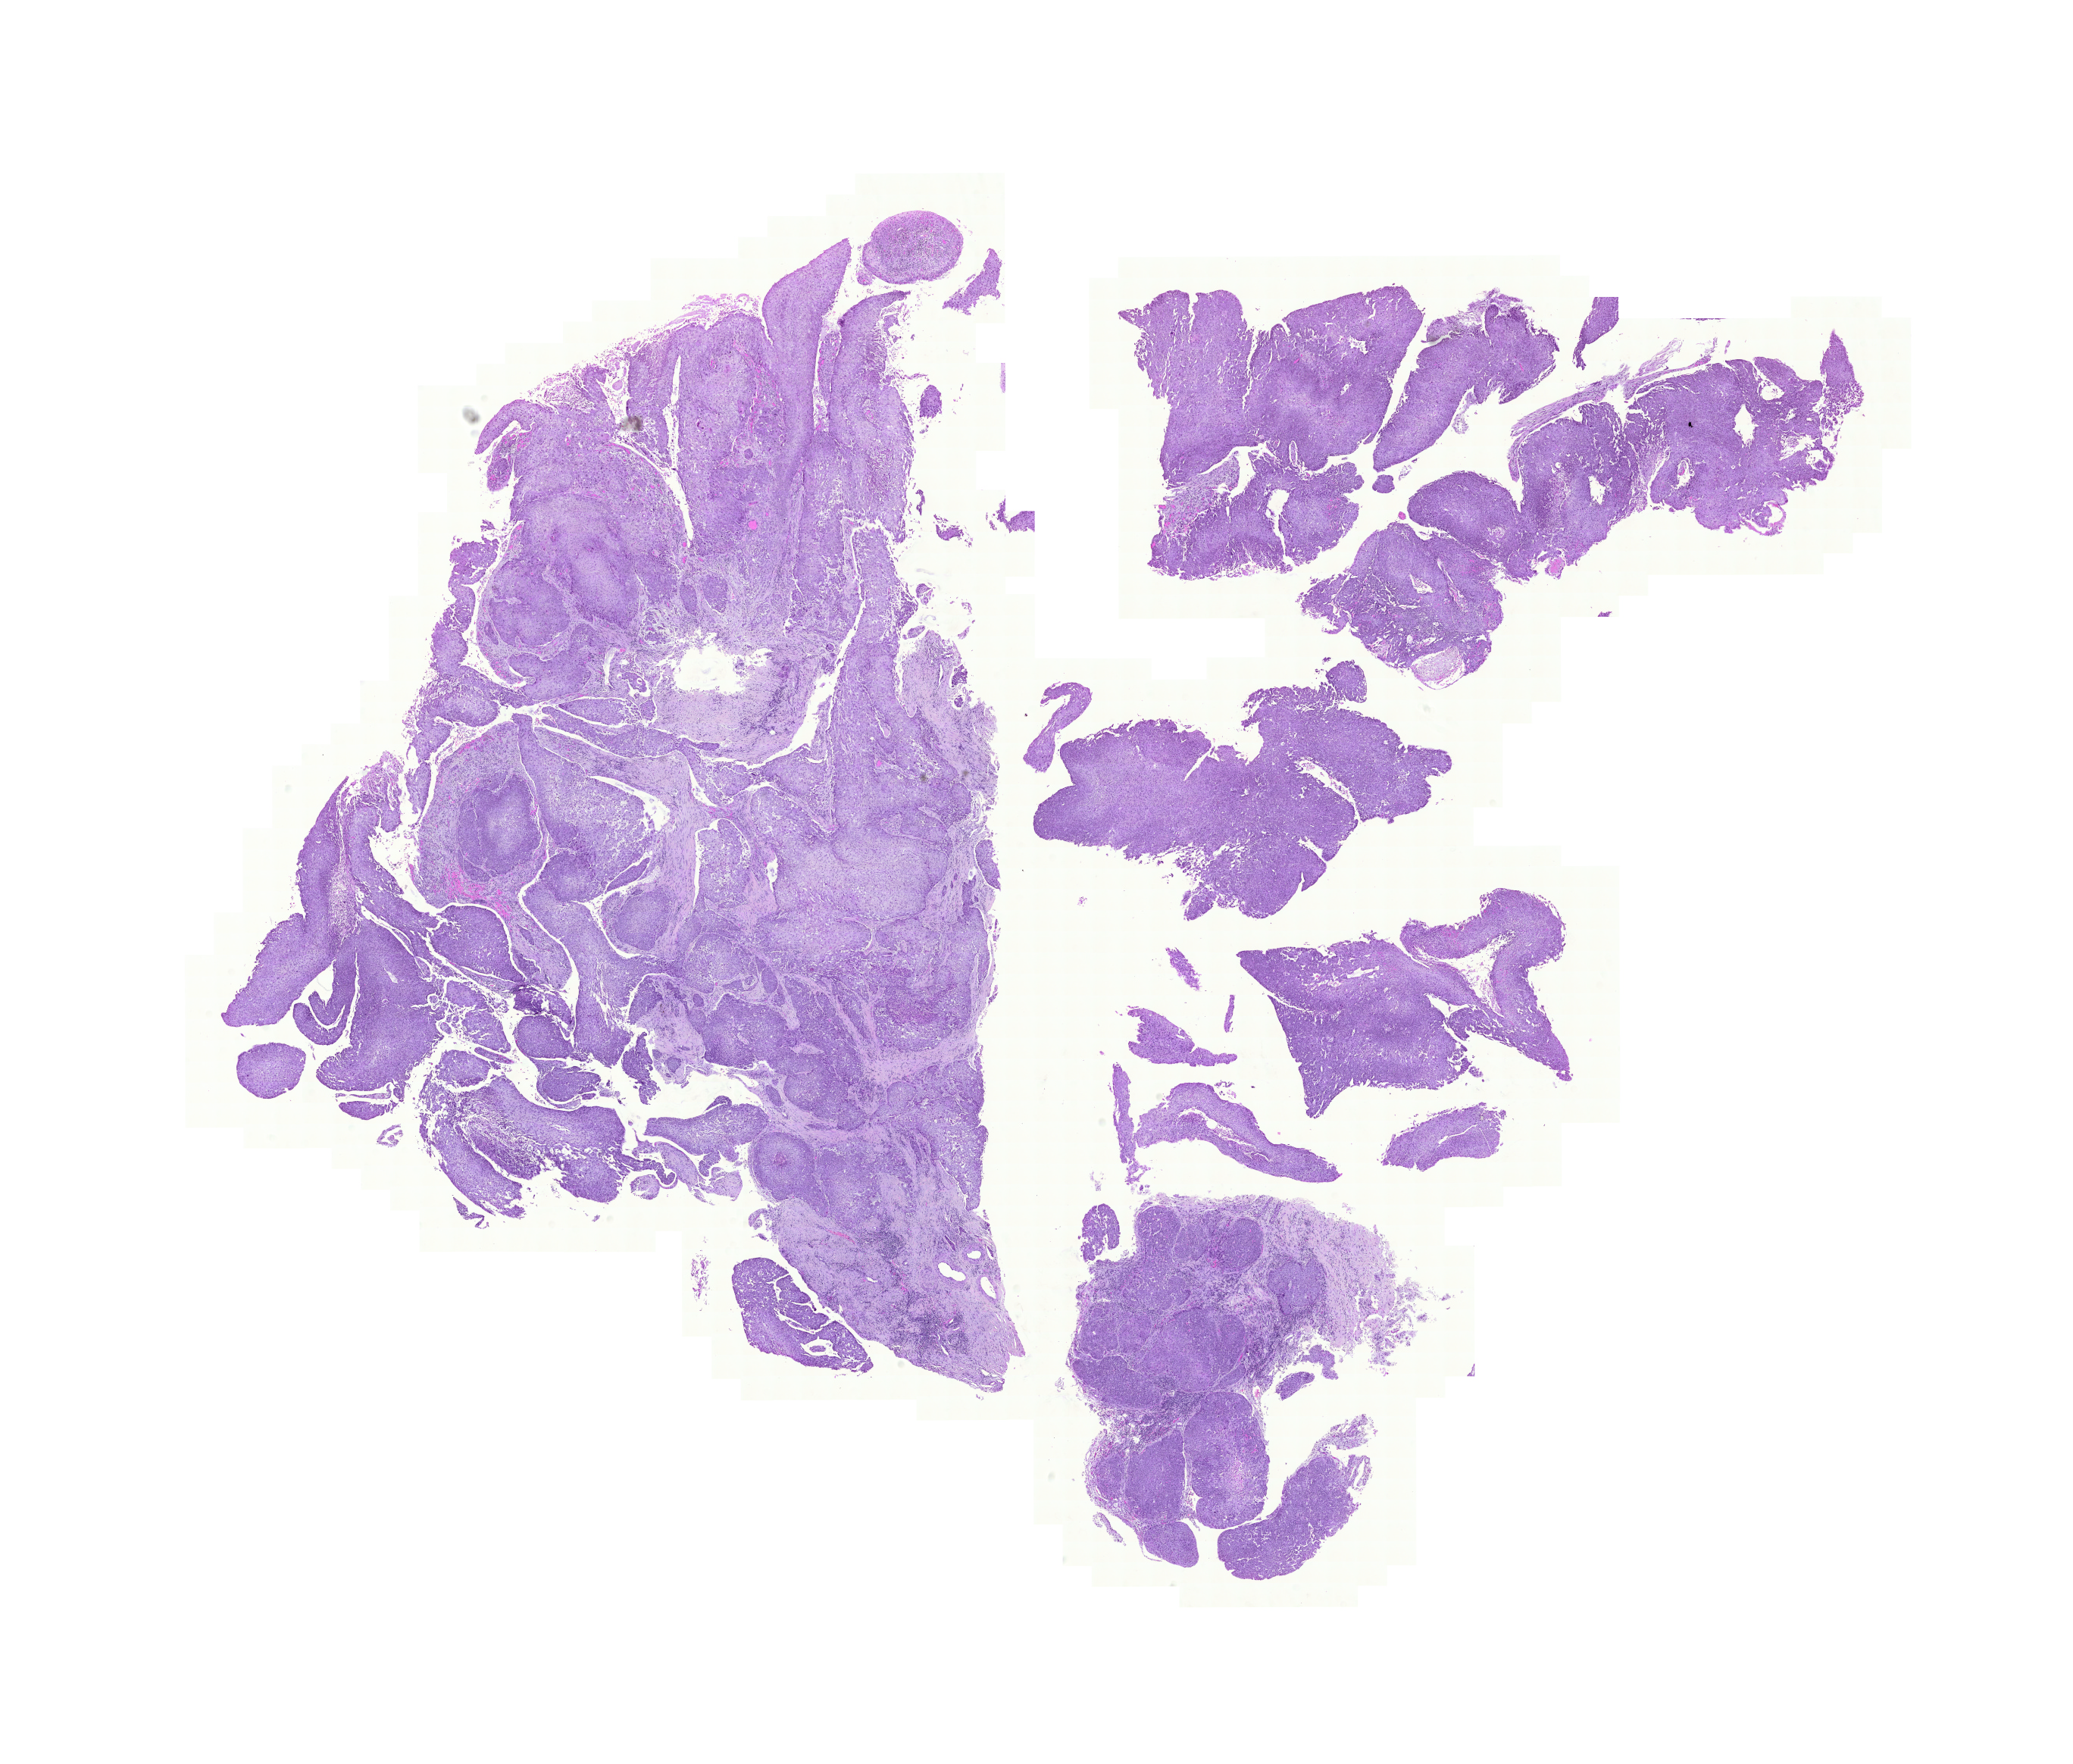
Digitized H&E-stained tissue section (whole slide), a low-resolution overview of the entire scanned area, about 20.4 x 17.3 mm (acquisition: 20x scan). Formalin-fixed paraffin-embedded (FFPE) diagnostic section. Sample: primary tumour, bladder. Male, age 71 years at initial diagnosis. Histologic grade: high grade.
AJCC pathologic stage: III (5th edition). Diagnosis: Transitional cell carcinoma. TNM: T3b N0 M0.